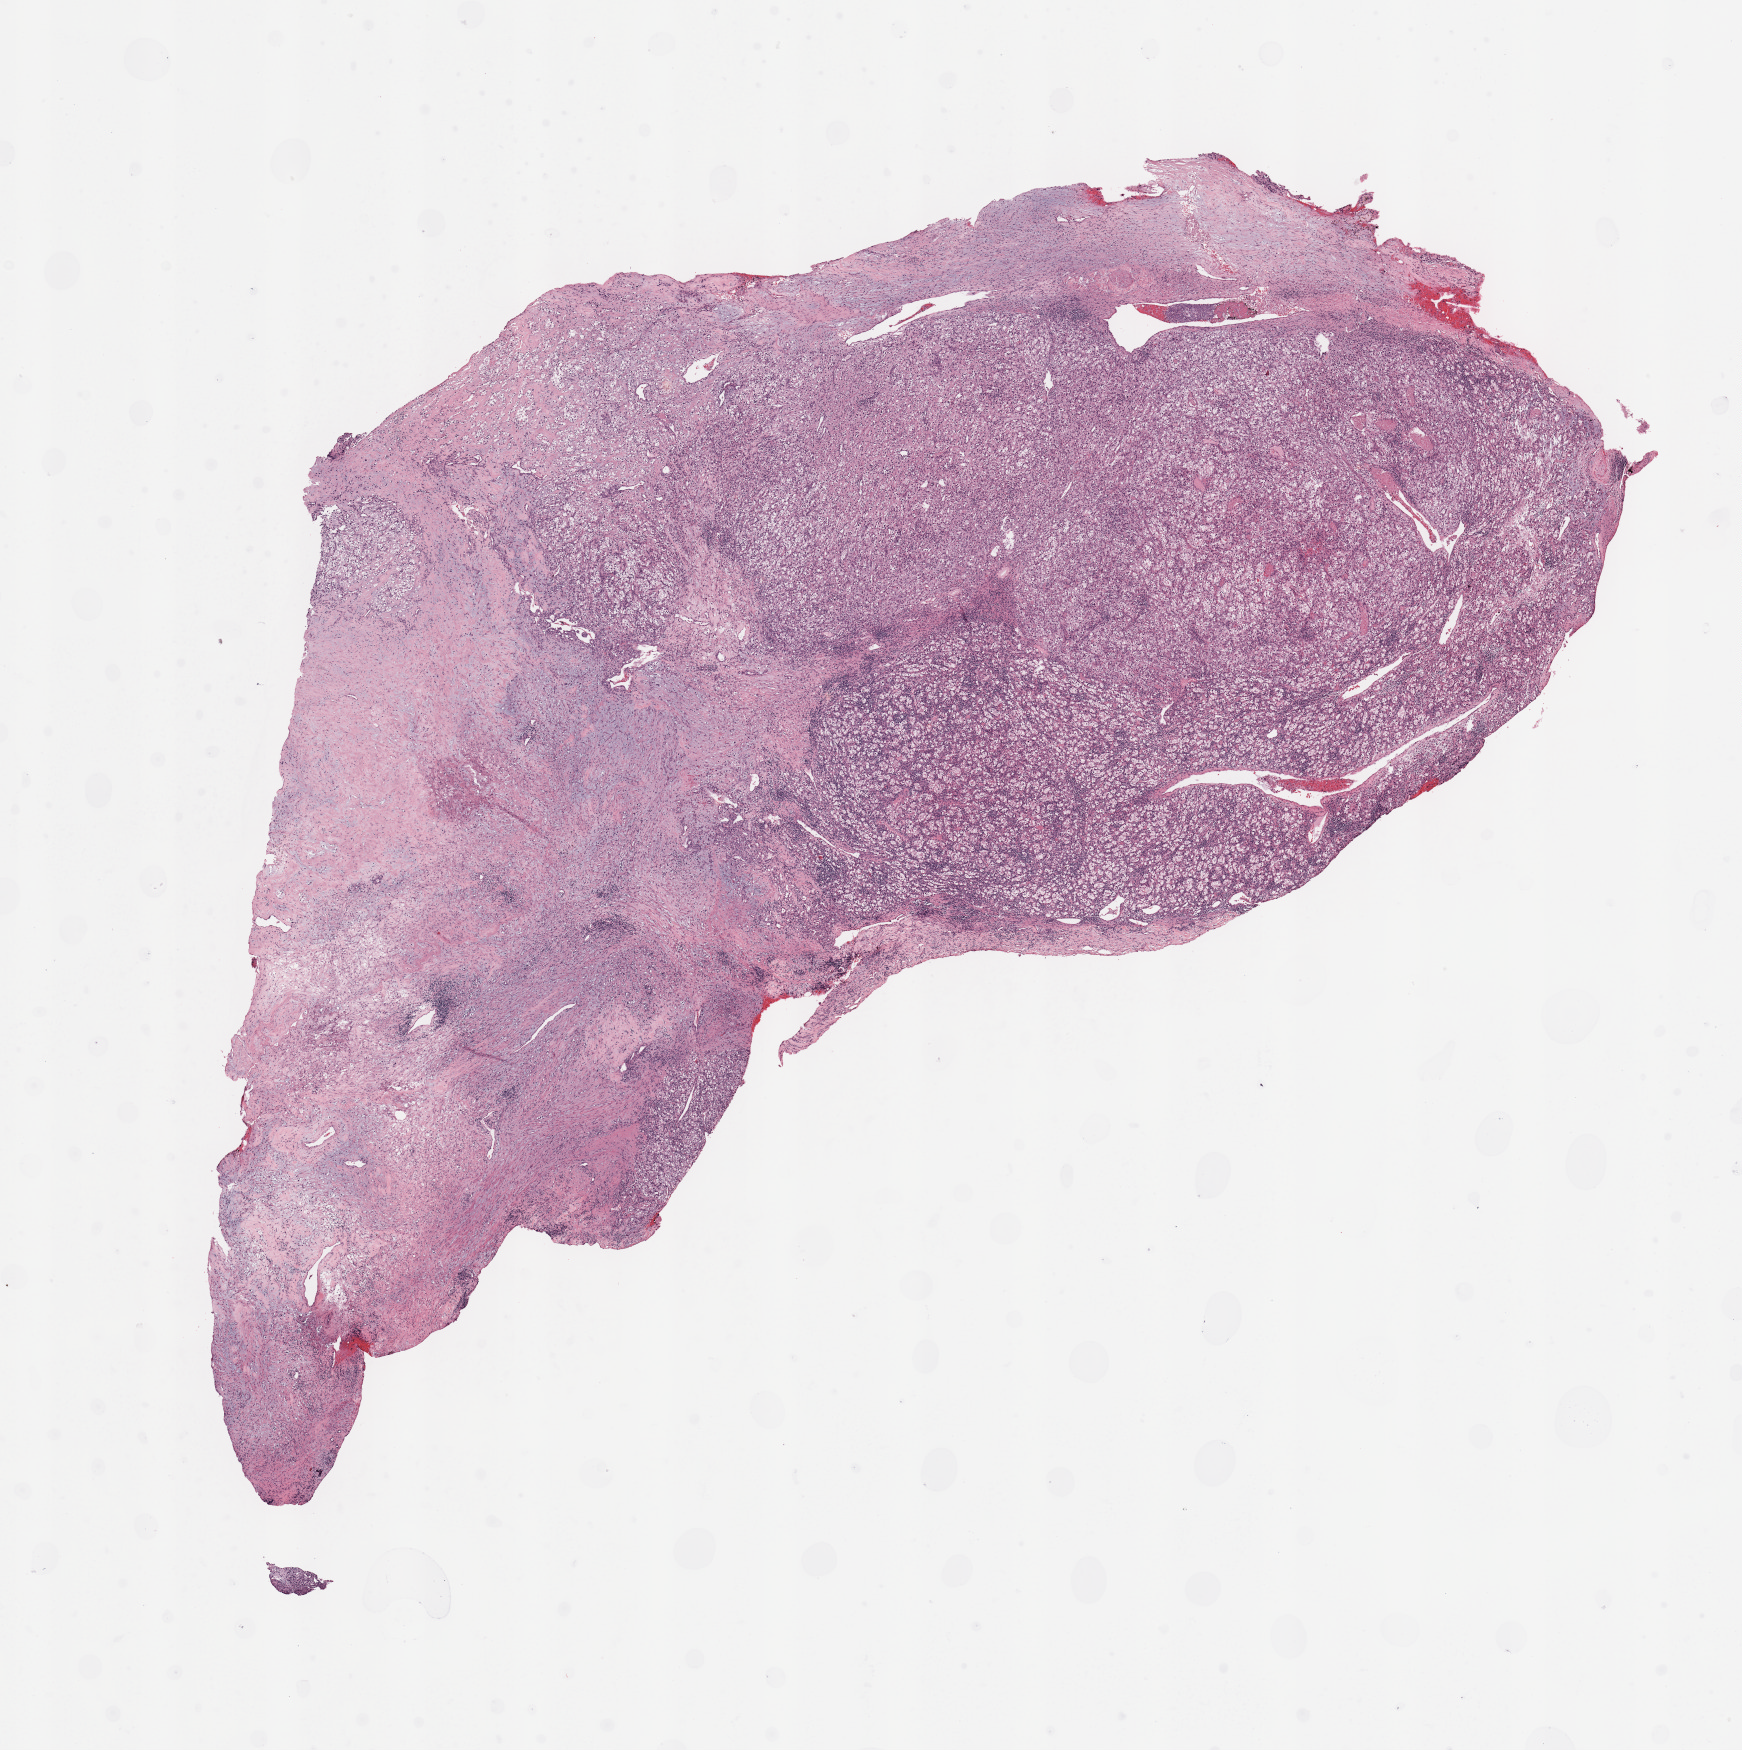
Digitized Hematoxylin and eosin (H&E) stained tissue section (whole slide), low-resolution overview of the scanned area, about 13.8 x 13.8 mm (slide scanned at 20x). Tumour tissue sample, kidney. 53-year-old male patient. Histologic grade: G3 (poorly differentiated).
Diagnosis: Renal cell carcinoma, NOS. AJCC pathologic stage: II. Primary tumour site (as recorded): middle.